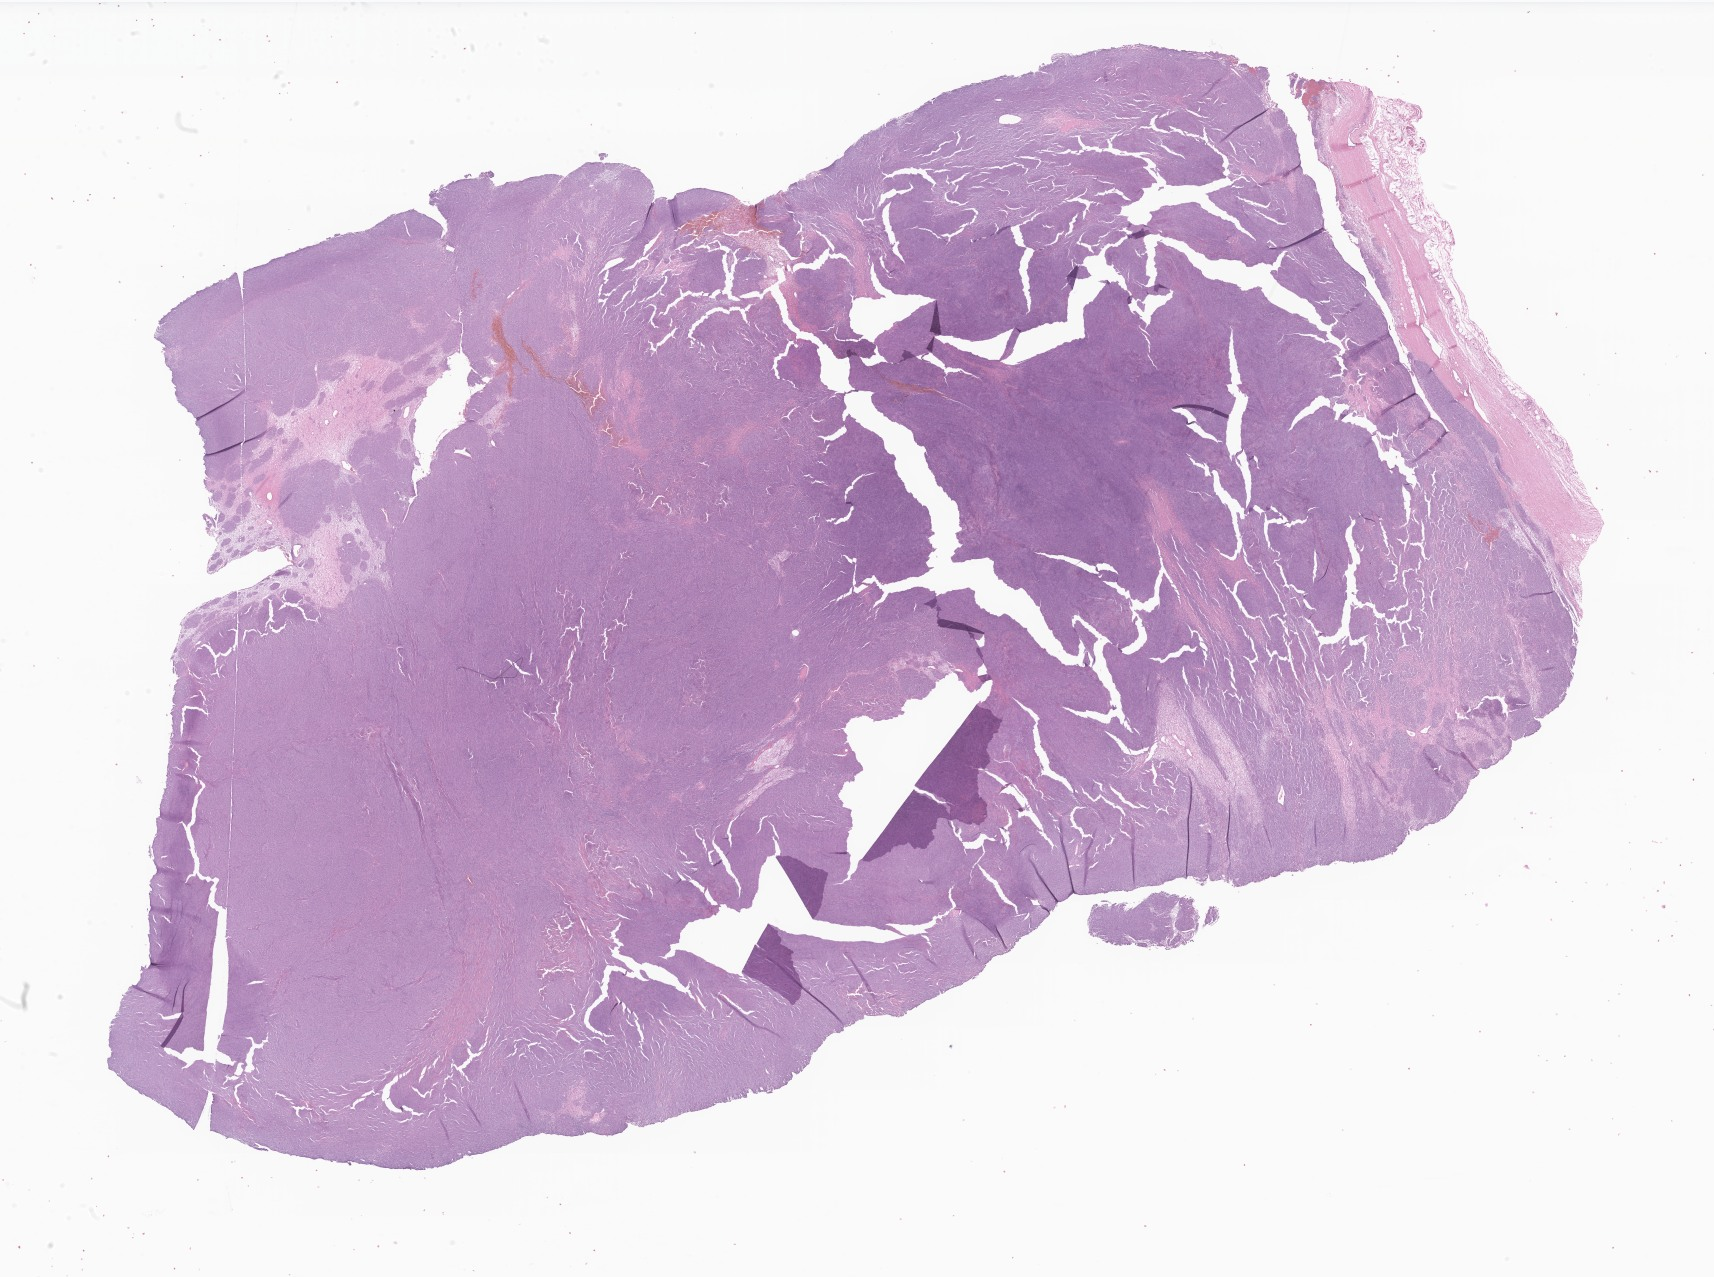
H&E whole-slide image of tumor tissue from the soft tissue of lower extremity, whole scanned area (about 28.9 x 21.5 mm) shown as a low-resolution overview; formalin-fixed paraffin-embedded section. Patient: male, age 276 months (23 years).
Diagnosis: Synovial sarcoma, NOS.